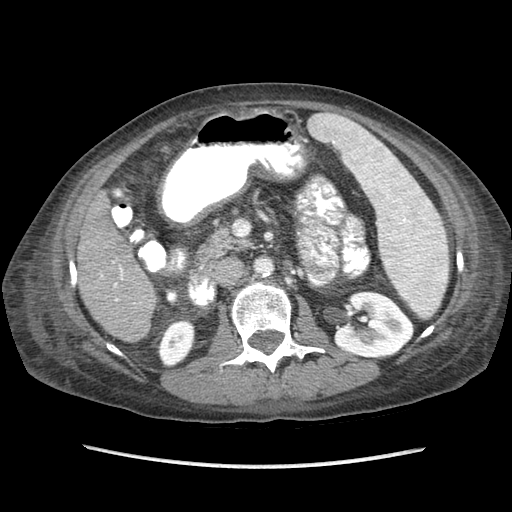
Contrast-enhanced abdominal CT (liver protocol), one axial slice; position 28 of 87 along the scan axis; soft-tissue window (W 400 / L 40 HU); 2.5 mm slice thickness; 512 × 512 image matrix, field of view 340 × 340 mm. Case-level facts recorded for this patient, not image findings: diagnosis: hepatocellular carcinoma (patient treated with transarterial chemoembolisation; whether this scan precedes or follows treatment is not stated here); TNM stage (as recorded): Stage-IIIB; Child-Pugh class: A; tumour differentiation: no biopsy; tumour nodularity: uninodular.
Annotated regions visible in this slice (semi-automatic segmentation, software-assisted and operator-edited):
- liver parenchyma outside the tumour (the mass and vessels are separate outlines, so this box may not span the whole liver): bounding box (x1, y1, x2, y2) in pixels: (77, 192, 156, 342)
- liver vessels: (101, 261, 123, 301)